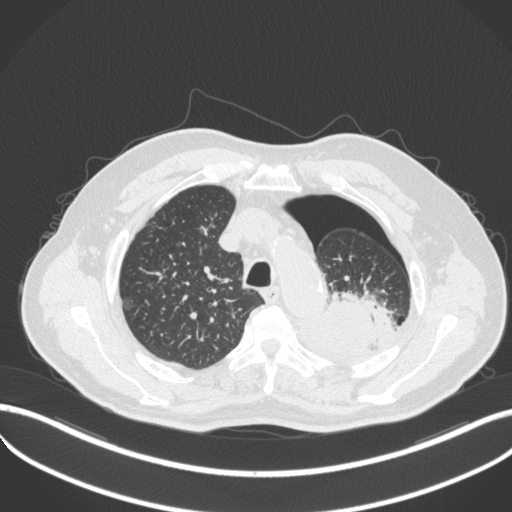
Chest CT, one axial slice. Slice 396 of 466 in the series (ordered by position). Reconstruction kernel B31f. 120 kVp. Lung window (W 1500 / L -600 HU). 512 × 512 image matrix, field of view 400 × 400 mm. Patient: male, 76 years. Case-level facts recorded for this patient, not image findings: clinical TNM (as recorded): T3 N0 M1b.
Annotated regions visible in this slice (rectangle marked by the reading radiologist):
- lung tumour (recorded histology: adenocarcinoma): box from (x=308, y=294) to (x=397, y=359) px